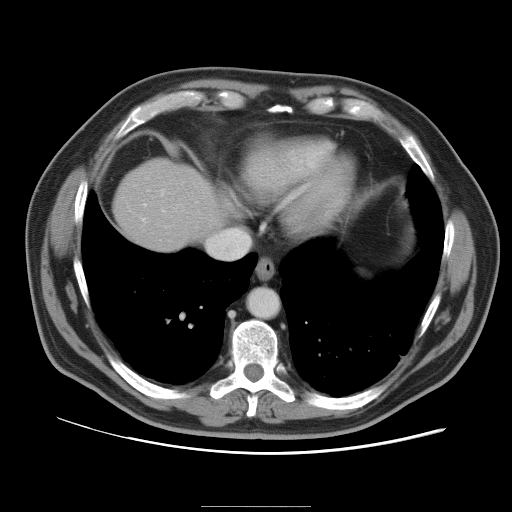
Contrast-enhanced abdominal CT, one axial slice. Intravenous contrast given. Soft-tissue window (W 400 / L 40 HU). 5 mm slice thickness. 512 × 512 image matrix, field of view 399 × 399 mm. Male patient, age 64 years. From the clinical record (not read from this slice): diagnosis: colorectal cancer liver metastases, imaged before liver resection; multiple liver metastases: yes; largest metastasis: 3 cm.
Annotated regions visible in this slice (outlined manually by an expert reader):
- hepatic veins: bounding box <142,218,145,221> (left, top, right, bottom; pixels)
- liver: <115,159,222,250>
- planned liver remnant (the part of the liver to remain after resection): <115,162,213,249>